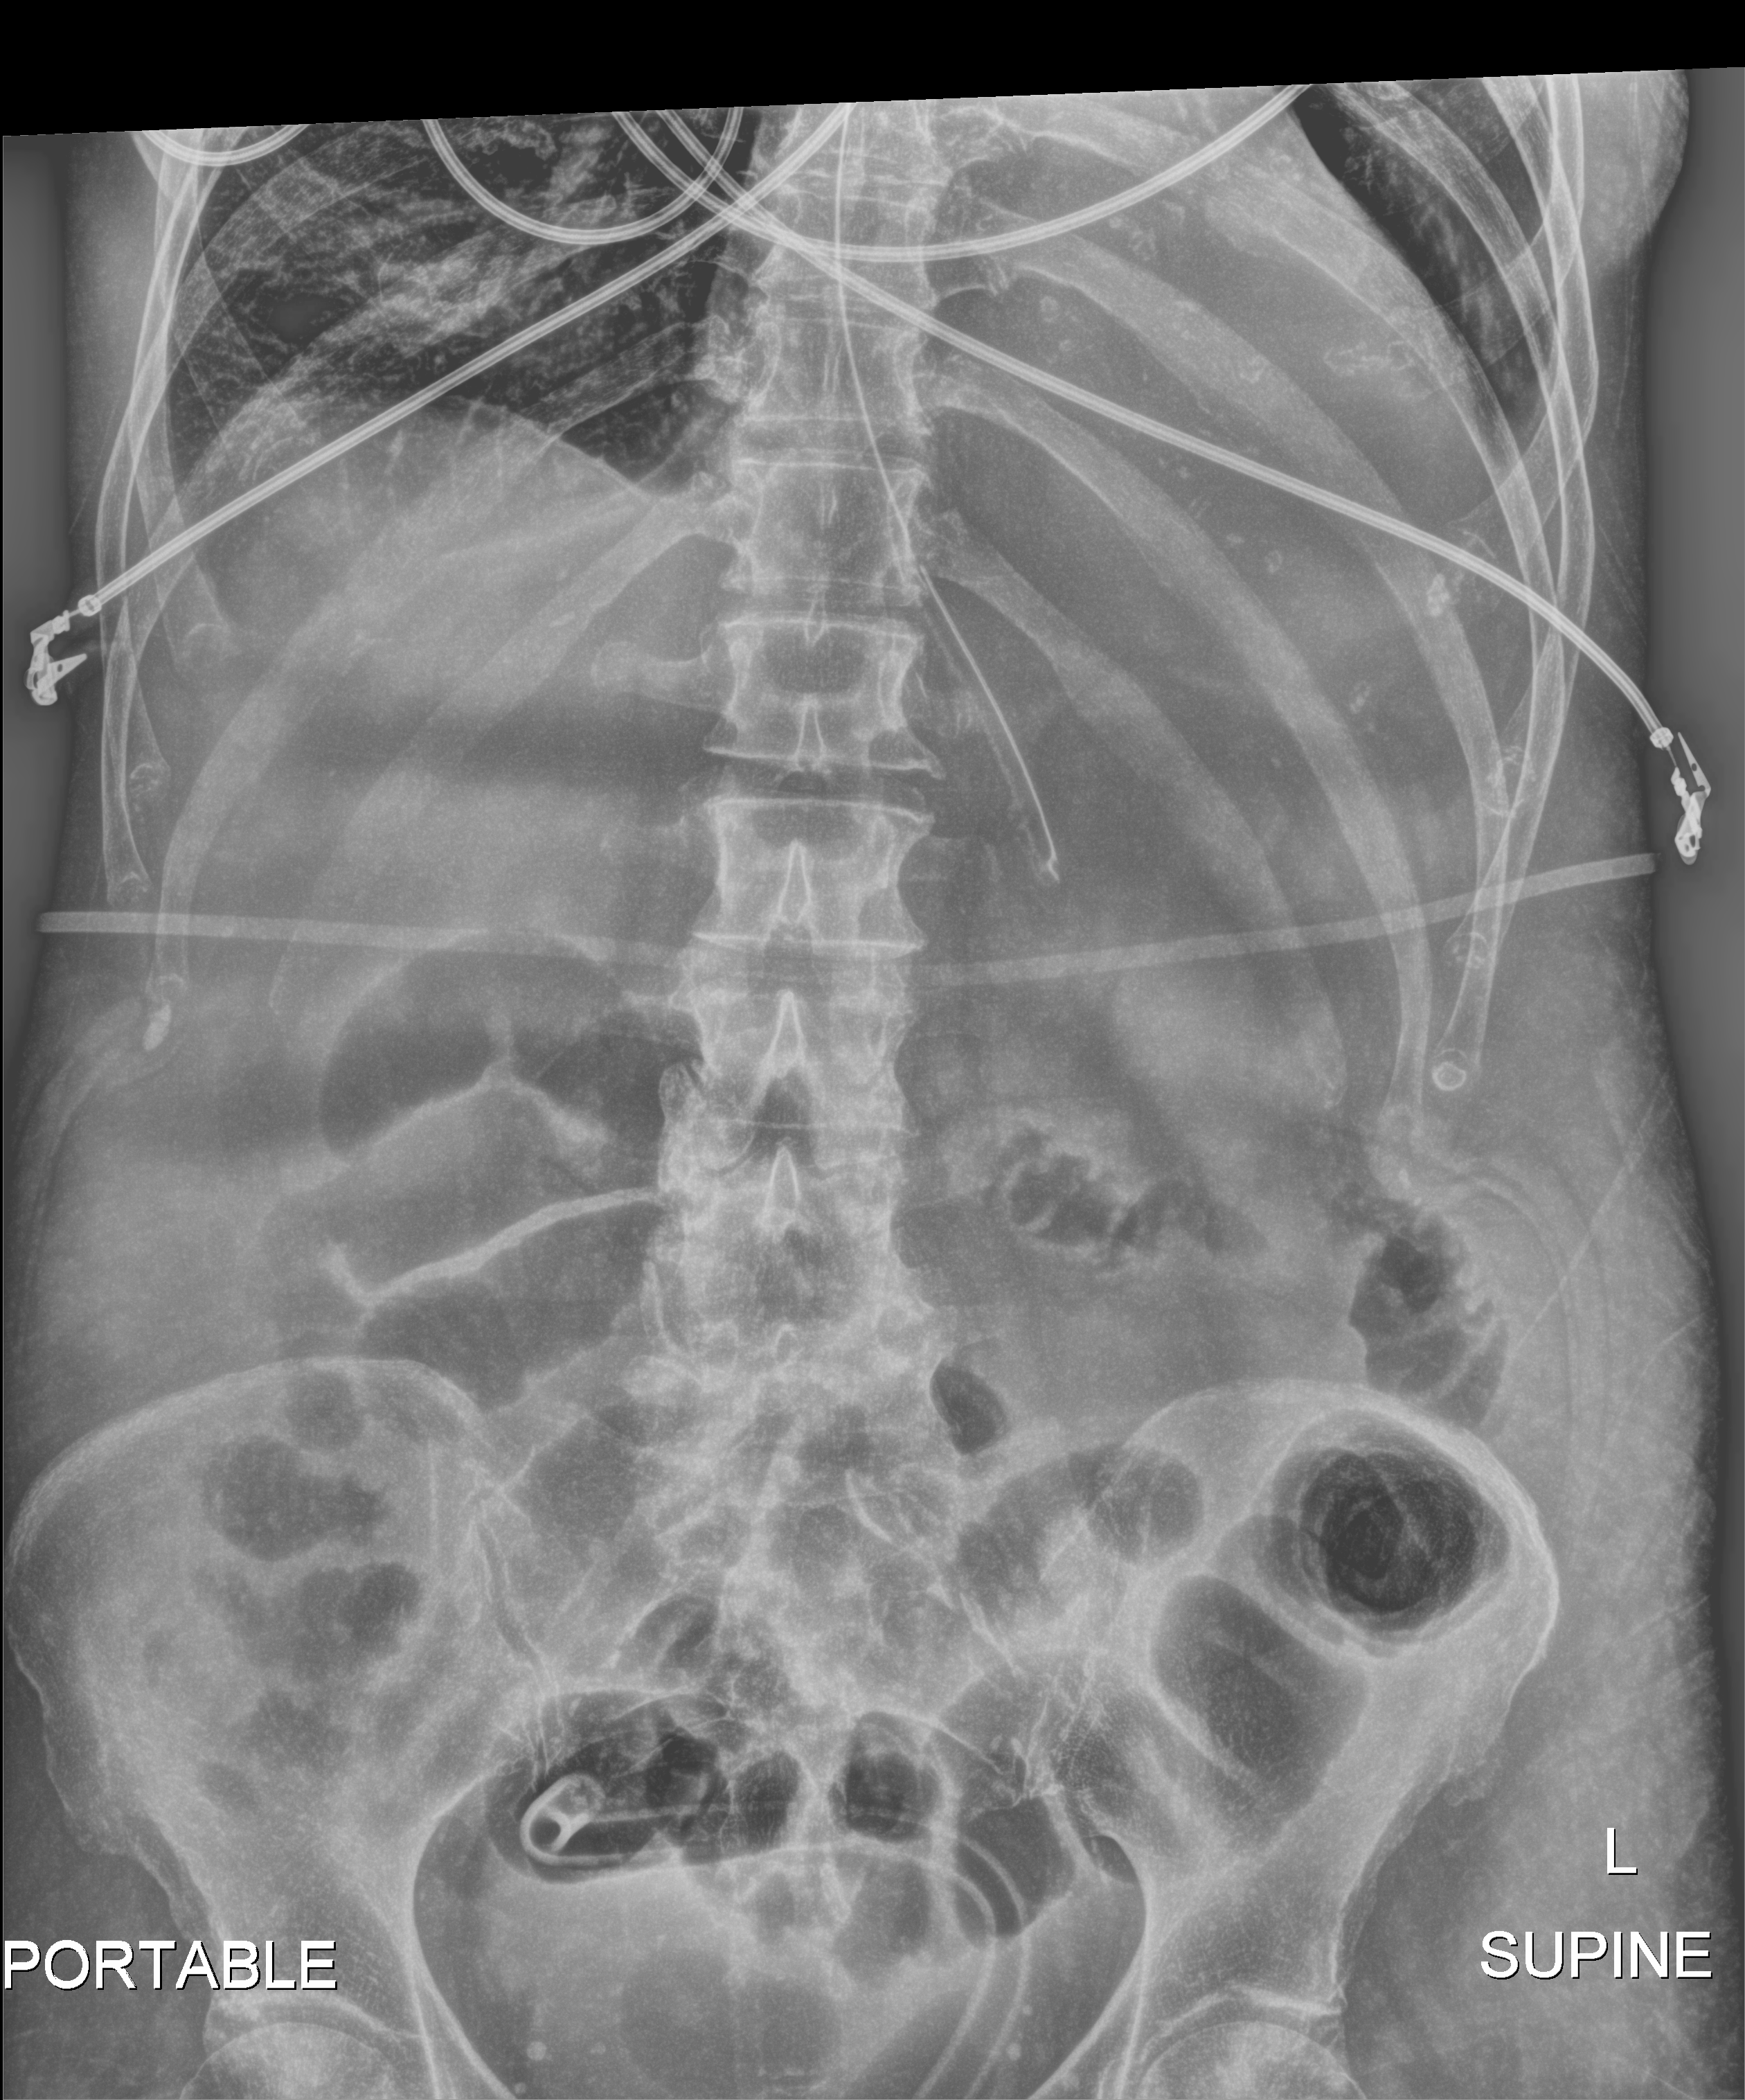
Bedside abdomen radiograph (digital radiography); anteroposterior (AP) projection. Female patient hospitalised with COVID-19, age 60–74 years.
Hospital-stay facts (about this admission, not read from this image; timing relative to this image not recorded): admitted to intensive care during this hospital stay: yes; mechanically ventilated during this hospital stay: yes.